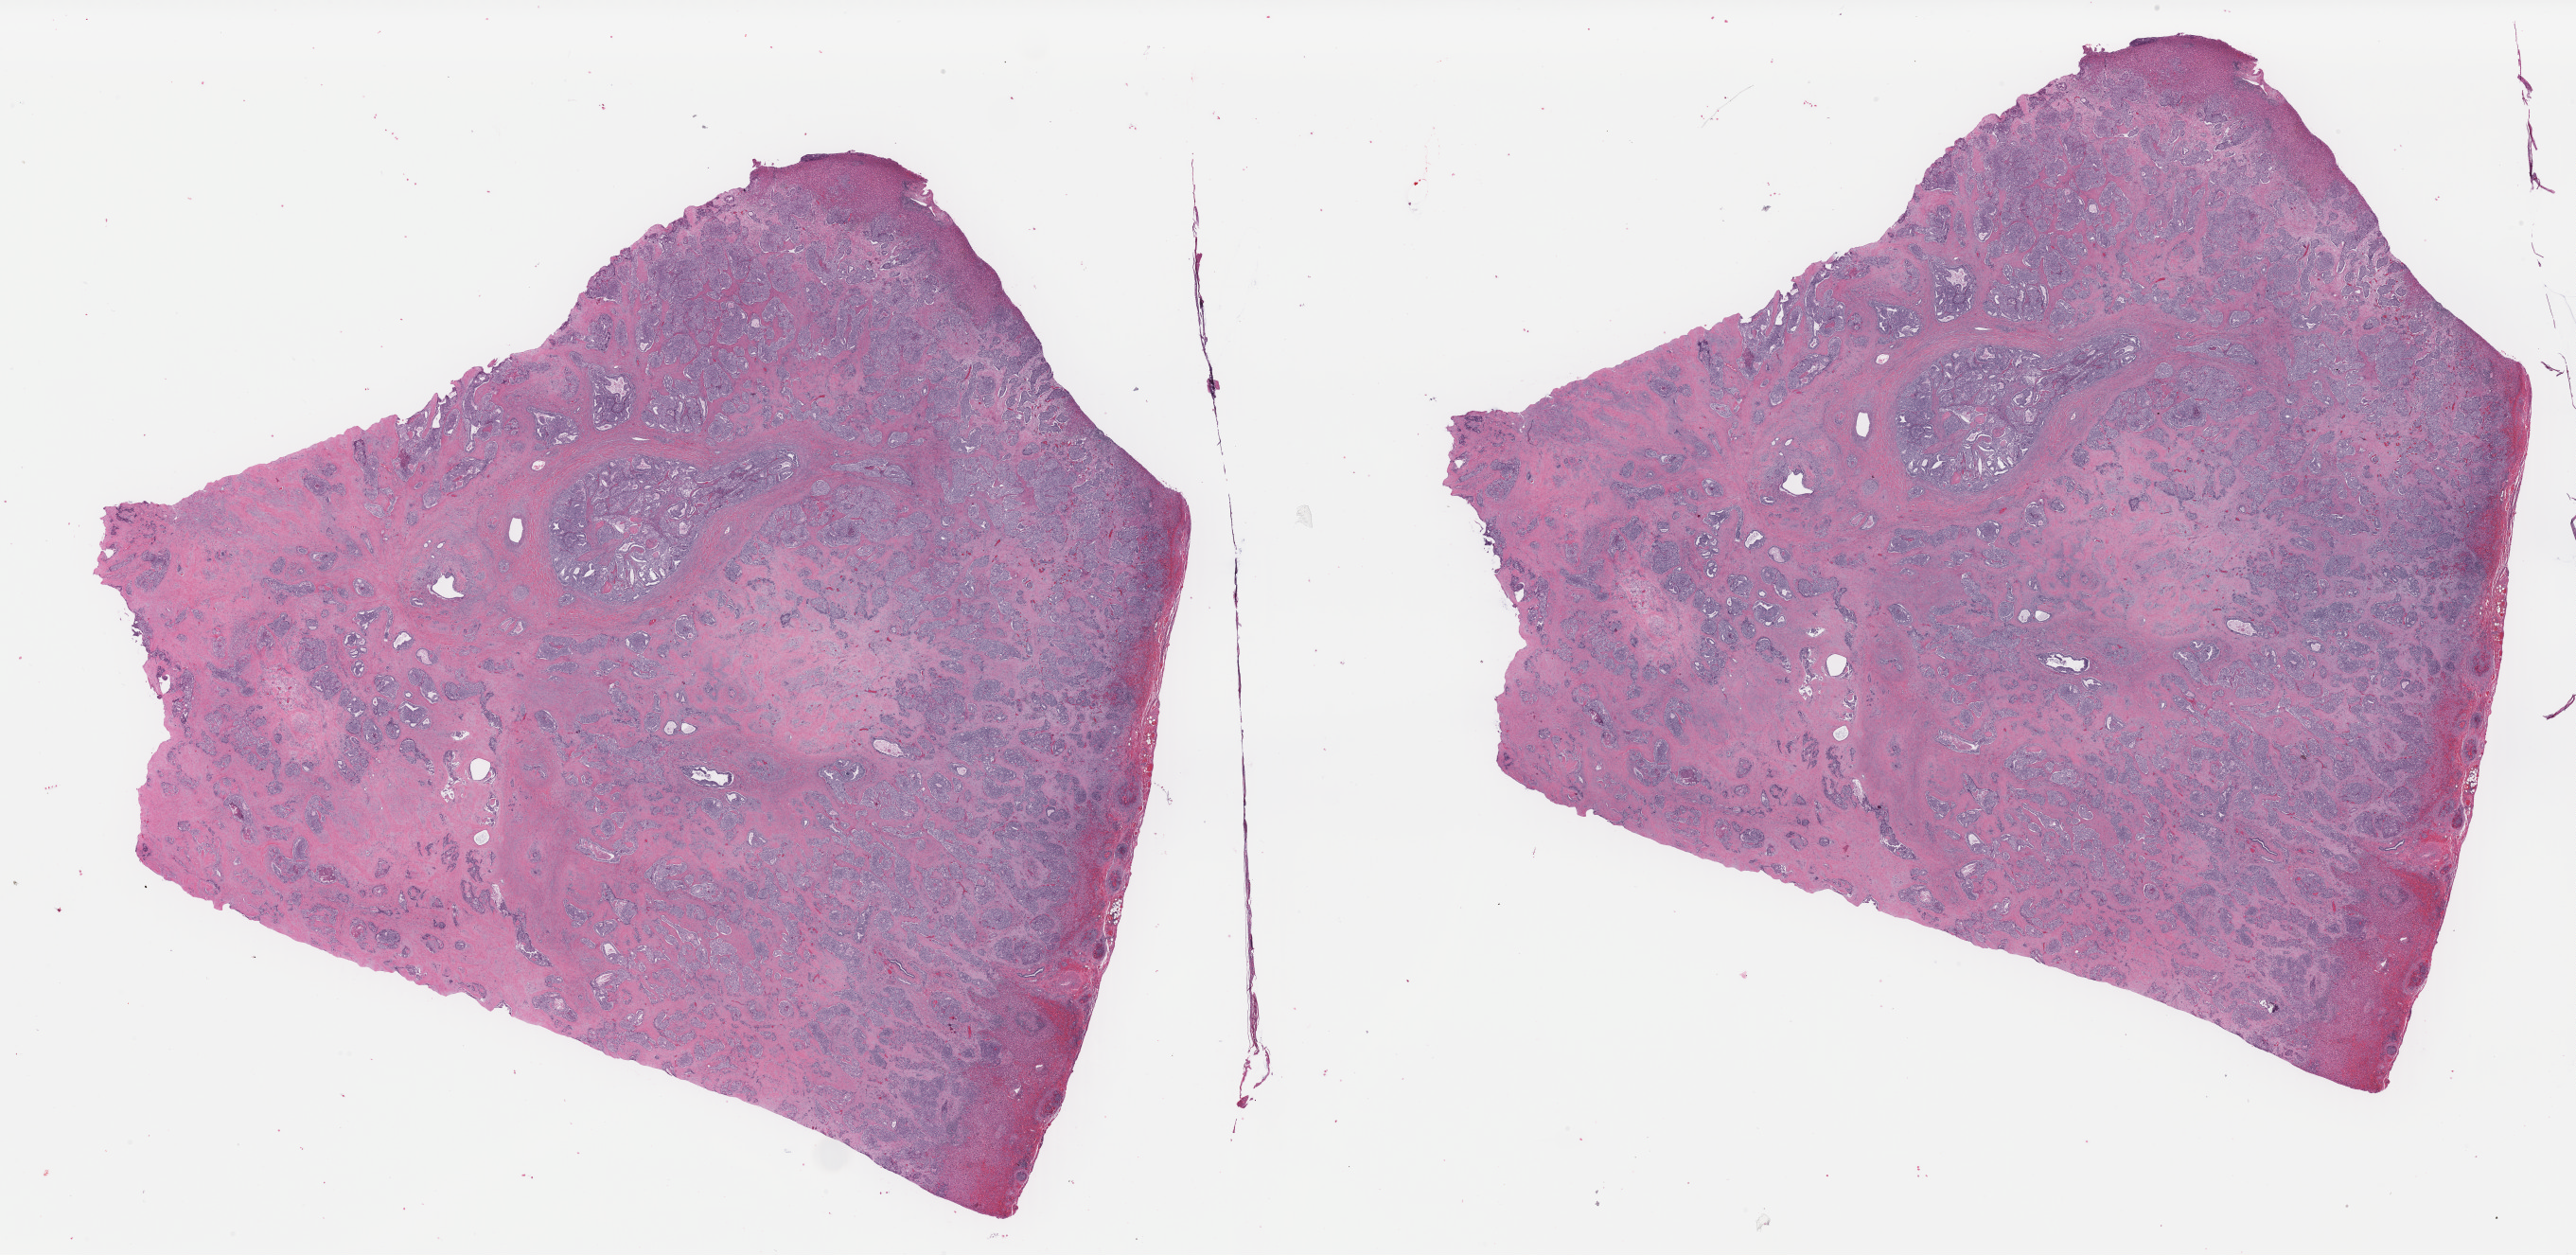
Digitized Hematoxylin and eosin (H&E) stained tissue section (whole slide) — whole scanned area (about 43.1 x 21.0 mm) shown as a low-resolution overview. Formalin-fixed paraffin-embedded (FFPE) diagnostic section. Primary tumour sample from the bile duct. Male patient; age at initial diagnosis 69 years. Histologic grade: G3 (poorly differentiated).
Pathologic diagnosis: Cholangiocarcinoma (intrahepatic bile duct). AJCC pathologic stage: IVB (7th edition).